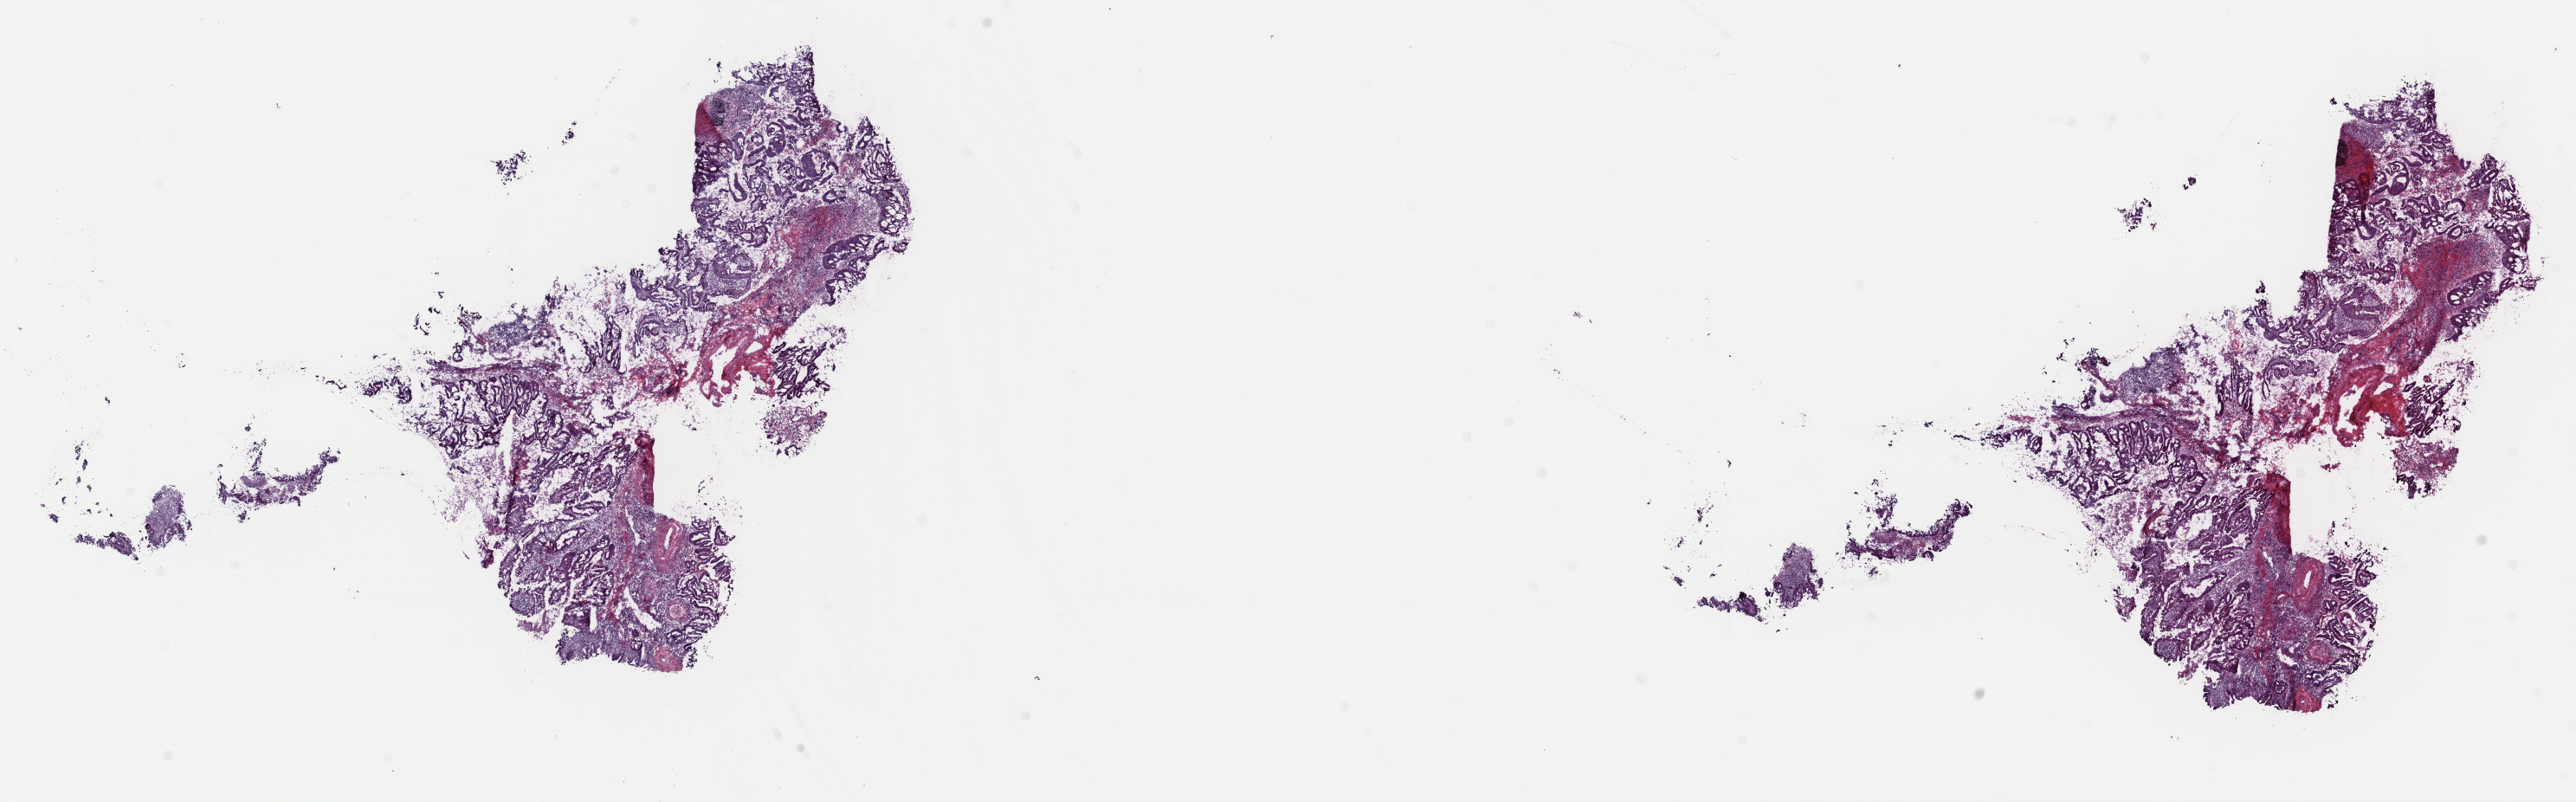
Digitized H&E-stained tissue section (whole slide), a low-resolution overview of the entire scanned area, about 23.5 x 7.3 mm (acquisition: 40x scan); frozen section from the top of the tissue portion; sample: primary tumour, cervix. Female, age 36 years at initial diagnosis. Histologic grade: G2 (moderately differentiated). Pathologist review of this section (percent, as recorded): tumour cells 60%, tumour nuclei 60%, normal cells 10%, stromal cells 30%, necrosis 0%. Infiltration values recorded for this section: lymphocyte infiltration 15%, monocyte infiltration 5%, neutrophil infiltration 5%.
Lymph nodes positive (case pathology): 0 of 2 examined. Diagnosis: Mucinous adenocarcinoma, endocervical type (endocervix). FIGO stage: IB1.